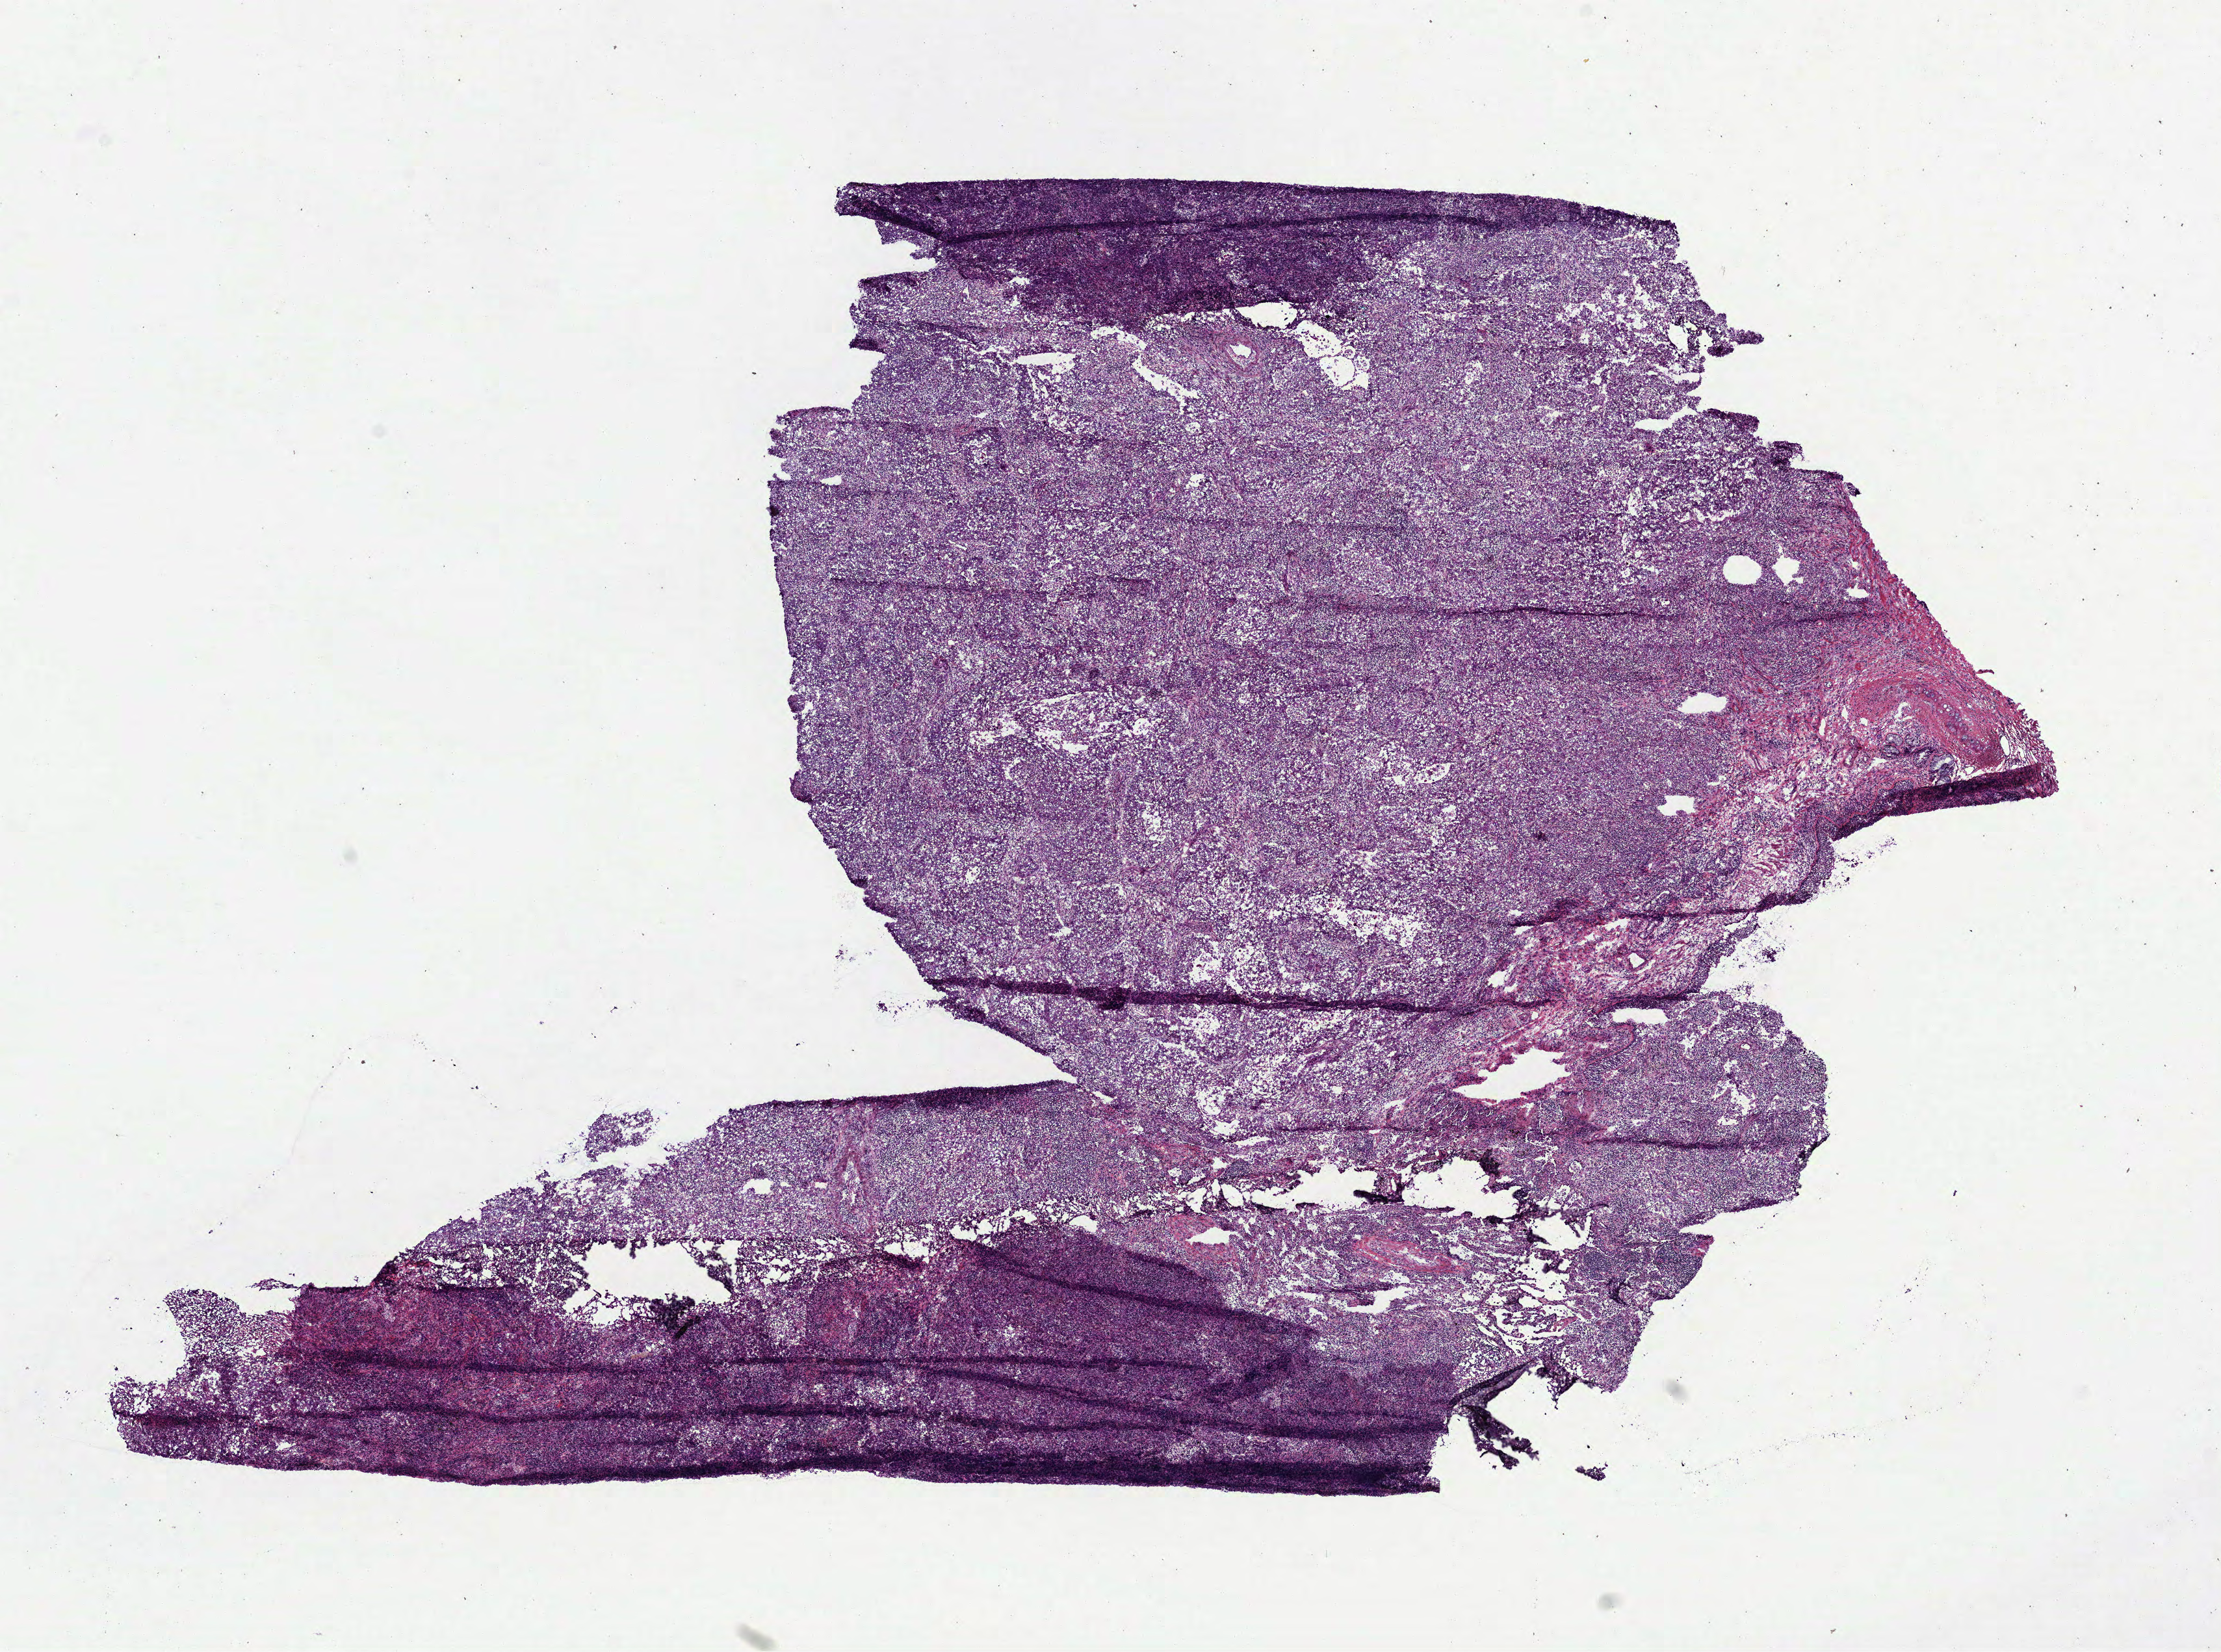
H&E-stained whole-slide image — whole scanned area (about 13.8 x 10.3 mm) shown as a low-resolution overview; frozen section; primary tumour sample from the lung. Patient: female, age at initial diagnosis 59 years. Slide review estimates, as recorded: tumour cells 87%, tumour nuclei 60%, normal cells 0%, stromal cells 10%, necrosis 2%.
• AJCC pathologic stage: IA (6th edition)
• diagnosis: Adenocarcinoma, NOS (upper lobe, lung)
• laterality: left